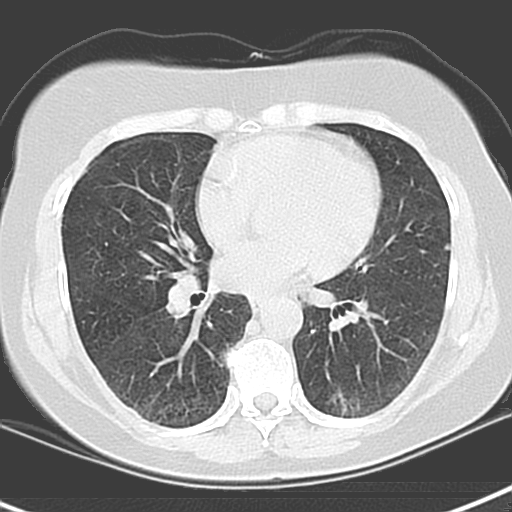
Low-dose screening chest CT, axial slice; first (baseline) screen; lung window (W 1500 / L -600 HU); 3.2 mm slice thickness; standard (soft-tissue) reconstruction kernel (B); 120 kVp; slice 77 of 129 in the series; 512 × 512 image matrix, field of view 290 × 290 mm. Female, age 55 years at enrolment. Current smoker at enrolment.
Lesion marked by an expert reader, bounding box <315,374,392,424> (left, top, right, bottom; pixels). The screening reader recorded 3 non-calcified nodules or masses ≥4 mm on this exam (left upper lobe, left lower lobe, left lower lobe); which of them this box marks is not recorded. Official screen result: positive, change unspecified: nodule(s) >= 4 mm or enlarging nodule(s), mass(es), or other non-specific abnormalities suspicious for lung cancer. Participant outcome: lung cancer diagnosed 1063 days after this screen (after the third annual screen) — adenocarcinoma with mixed subtypes, left lower lobe, poorly differentiated (G3), stage IA (AJCC 6th edition), 21 mm at pathology.